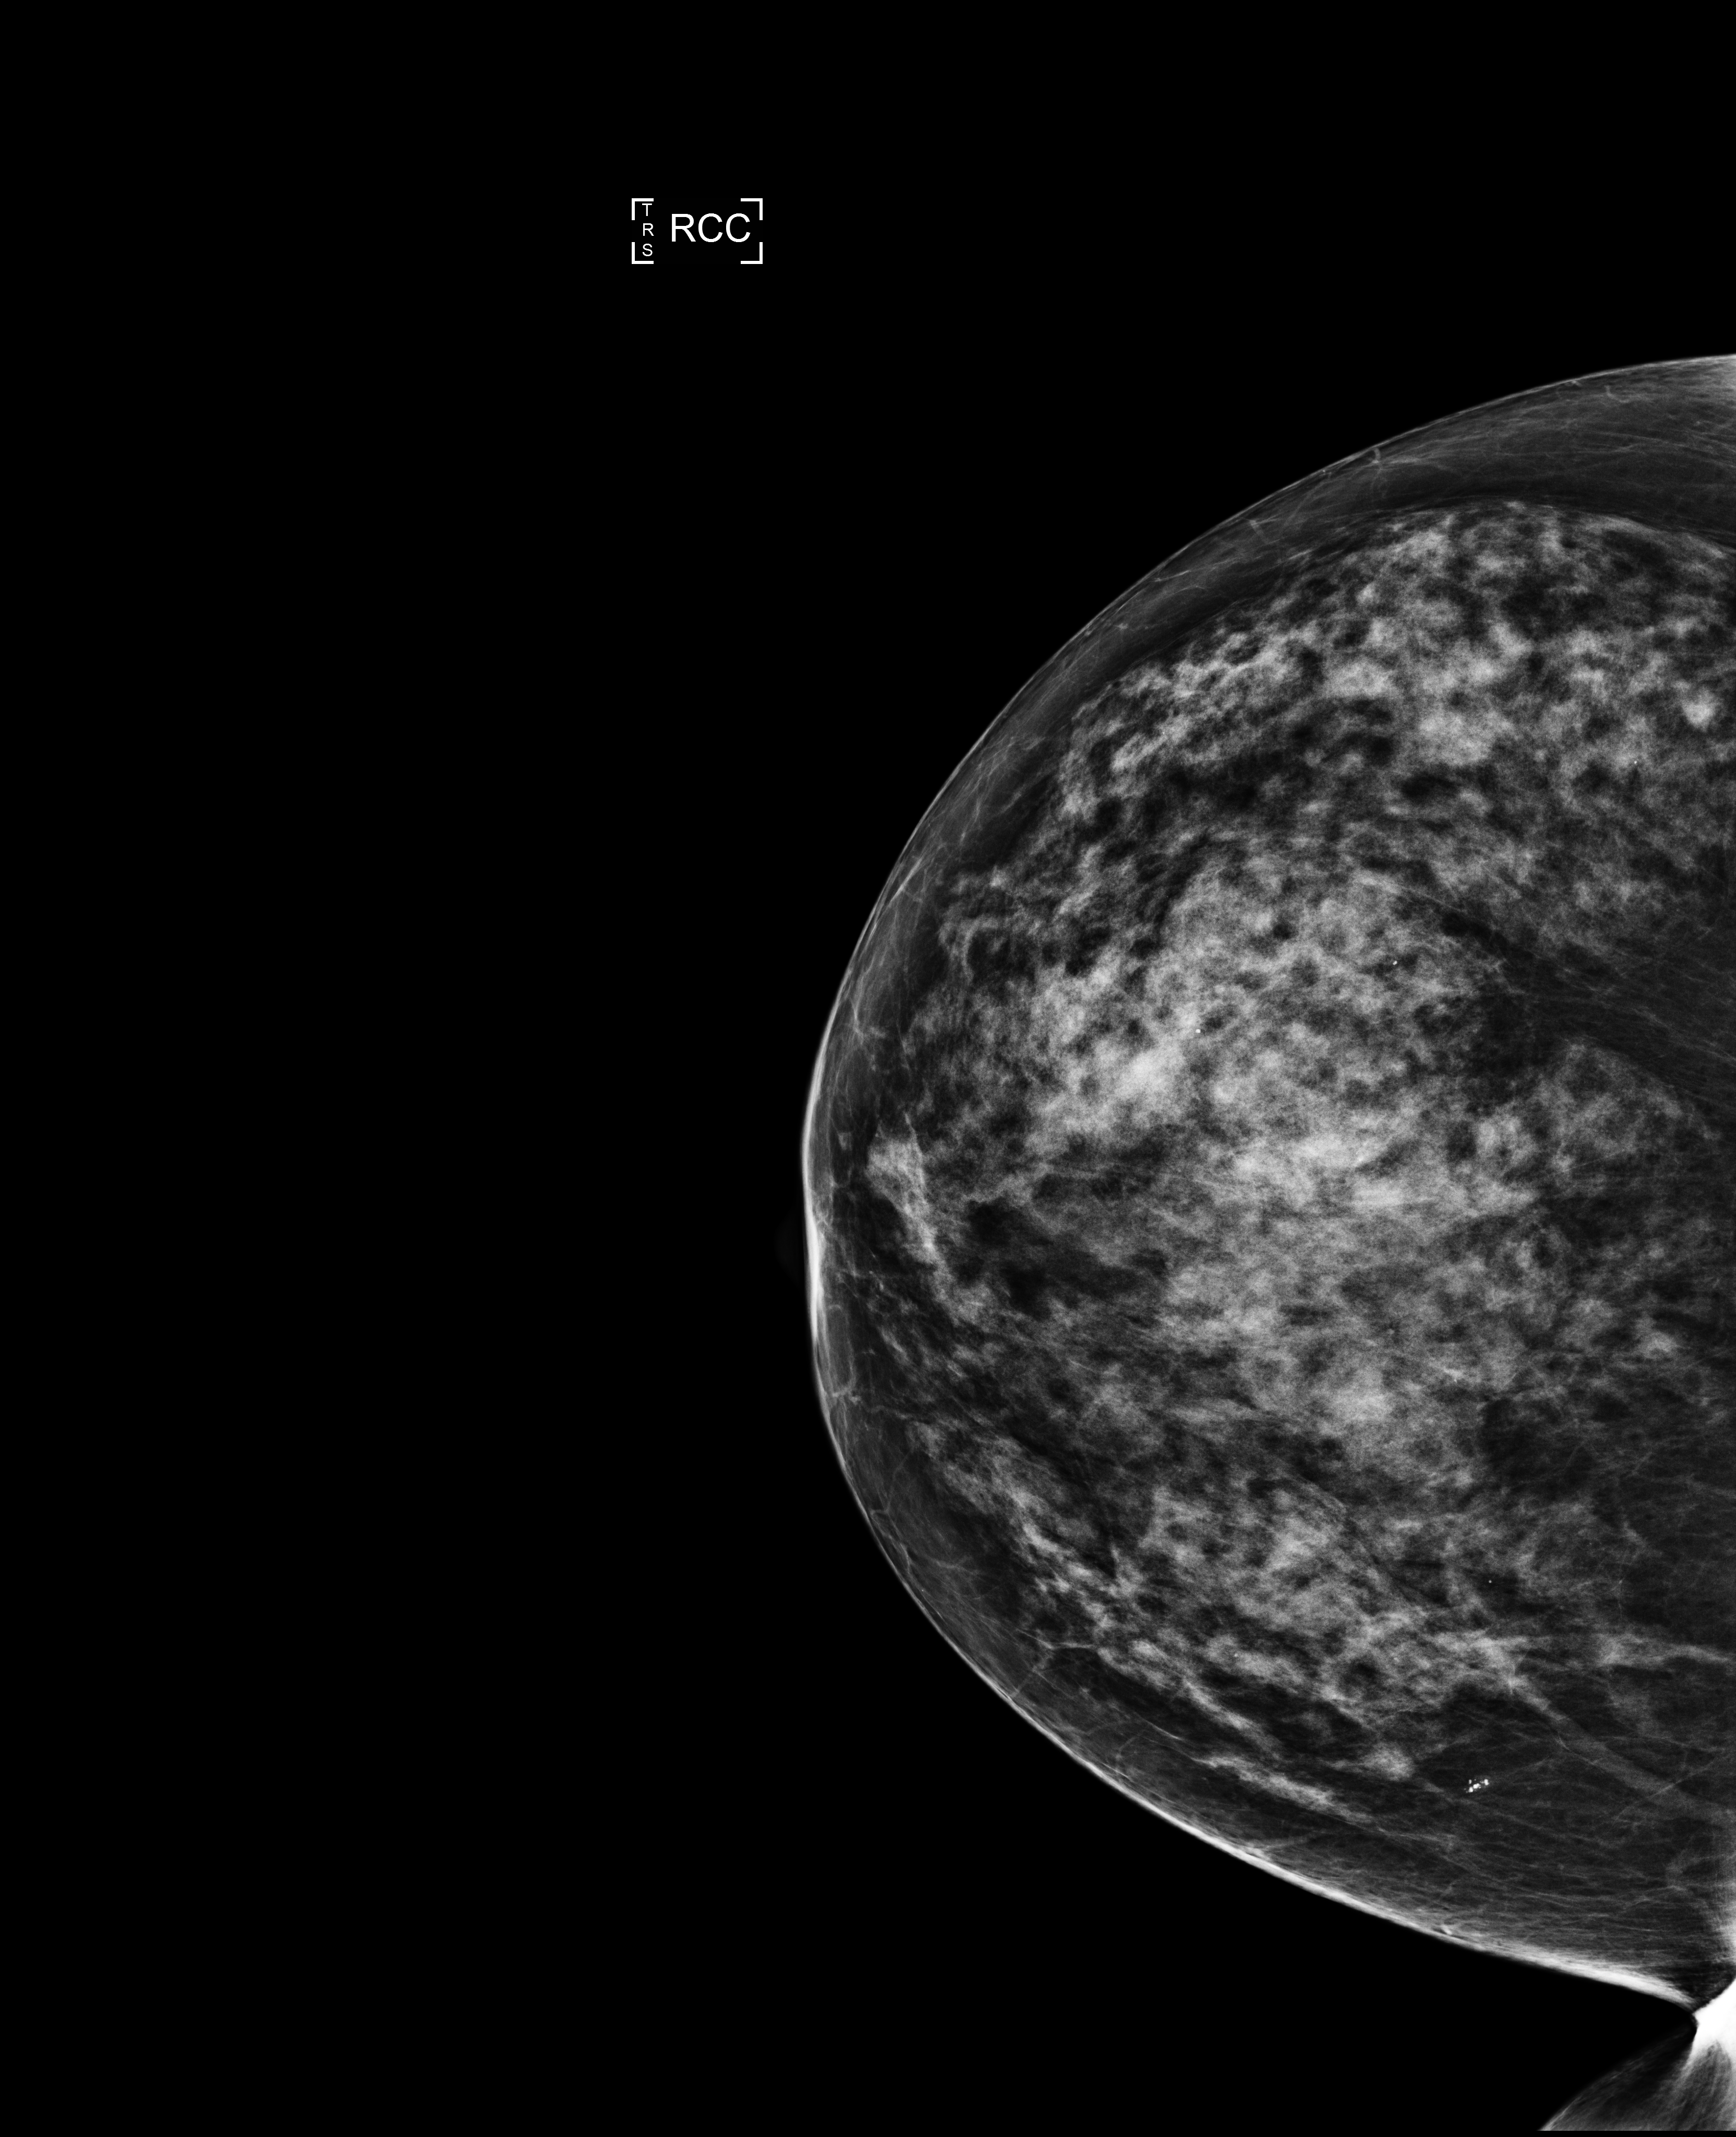
Annual screening mammography examination, compressed breast thickness 56 mm, system: Selenia Dimensions. Female patient, age 63 years.
Image type: full-field digital mammogram. Breast: right. Projection: cranio-caudal projection.